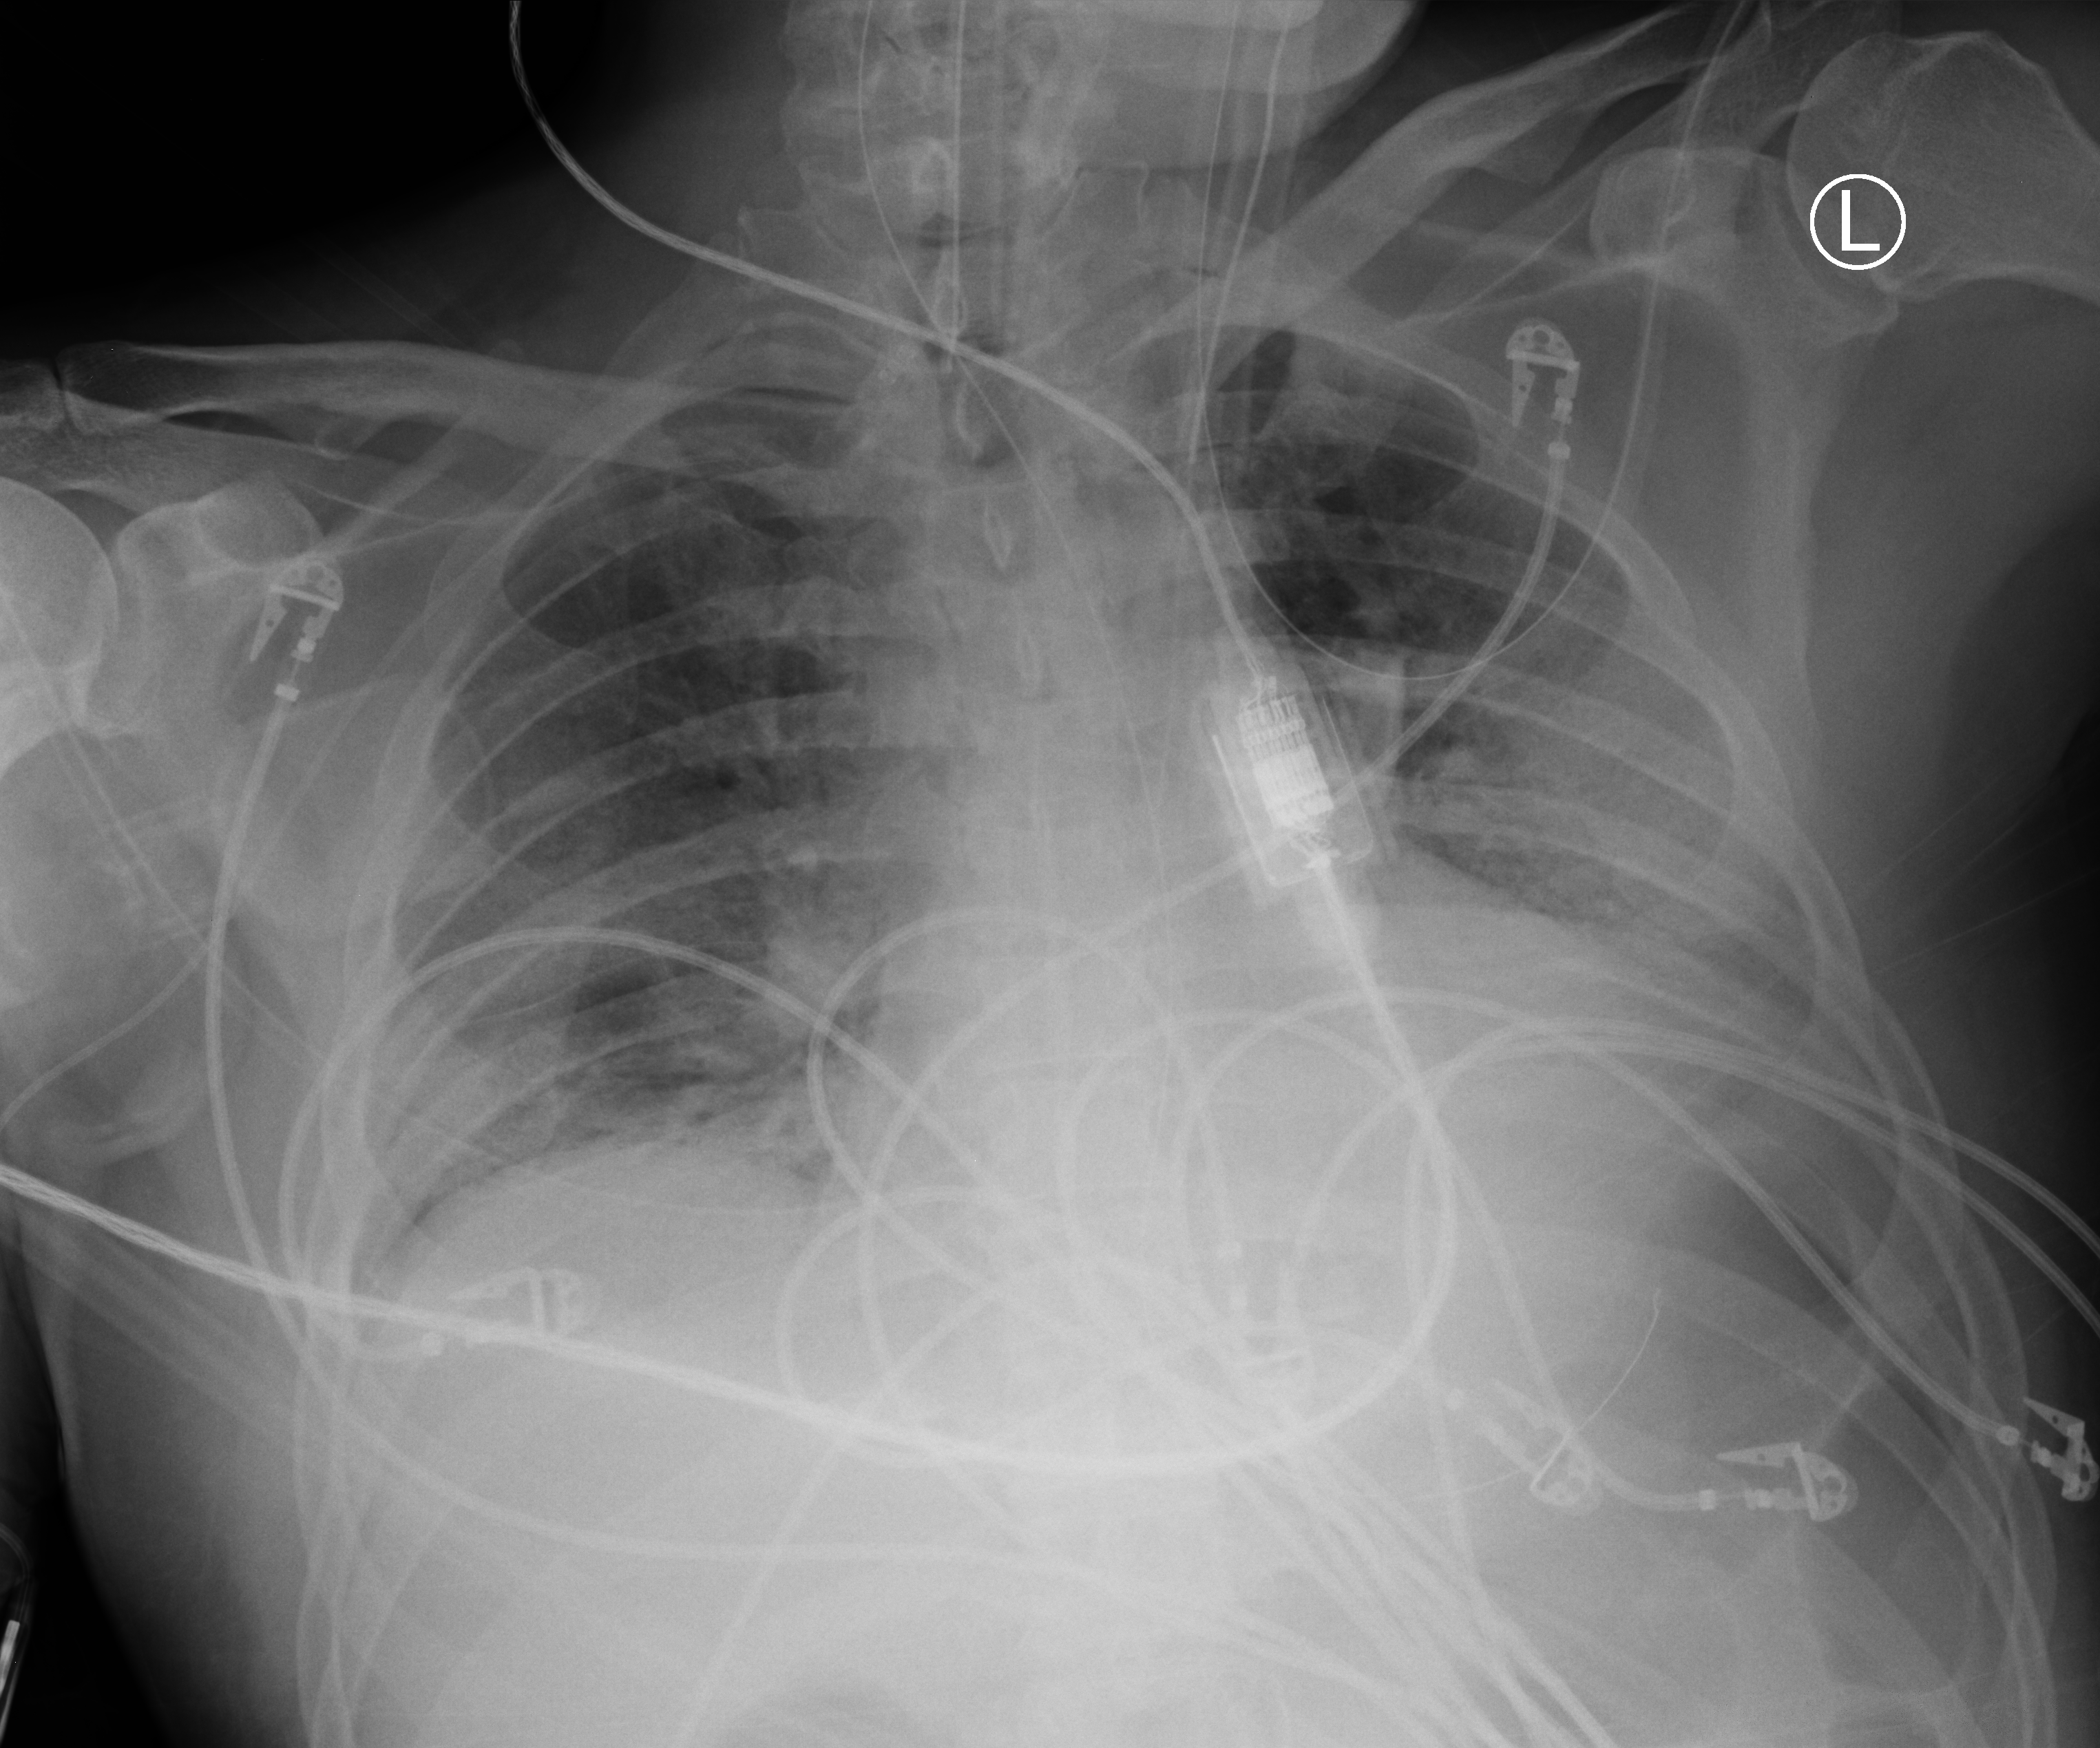
Bedside chest radiograph (computed radiography), anteroposterior (AP) projection. Patient hospitalised with COVID-19; male, aged 60–74 years.
Admission-level facts for this patient (not findings on this image; timing relative to this image not recorded):
- length of hospital stay: 26 days
- mechanically ventilated during this hospital stay: yes